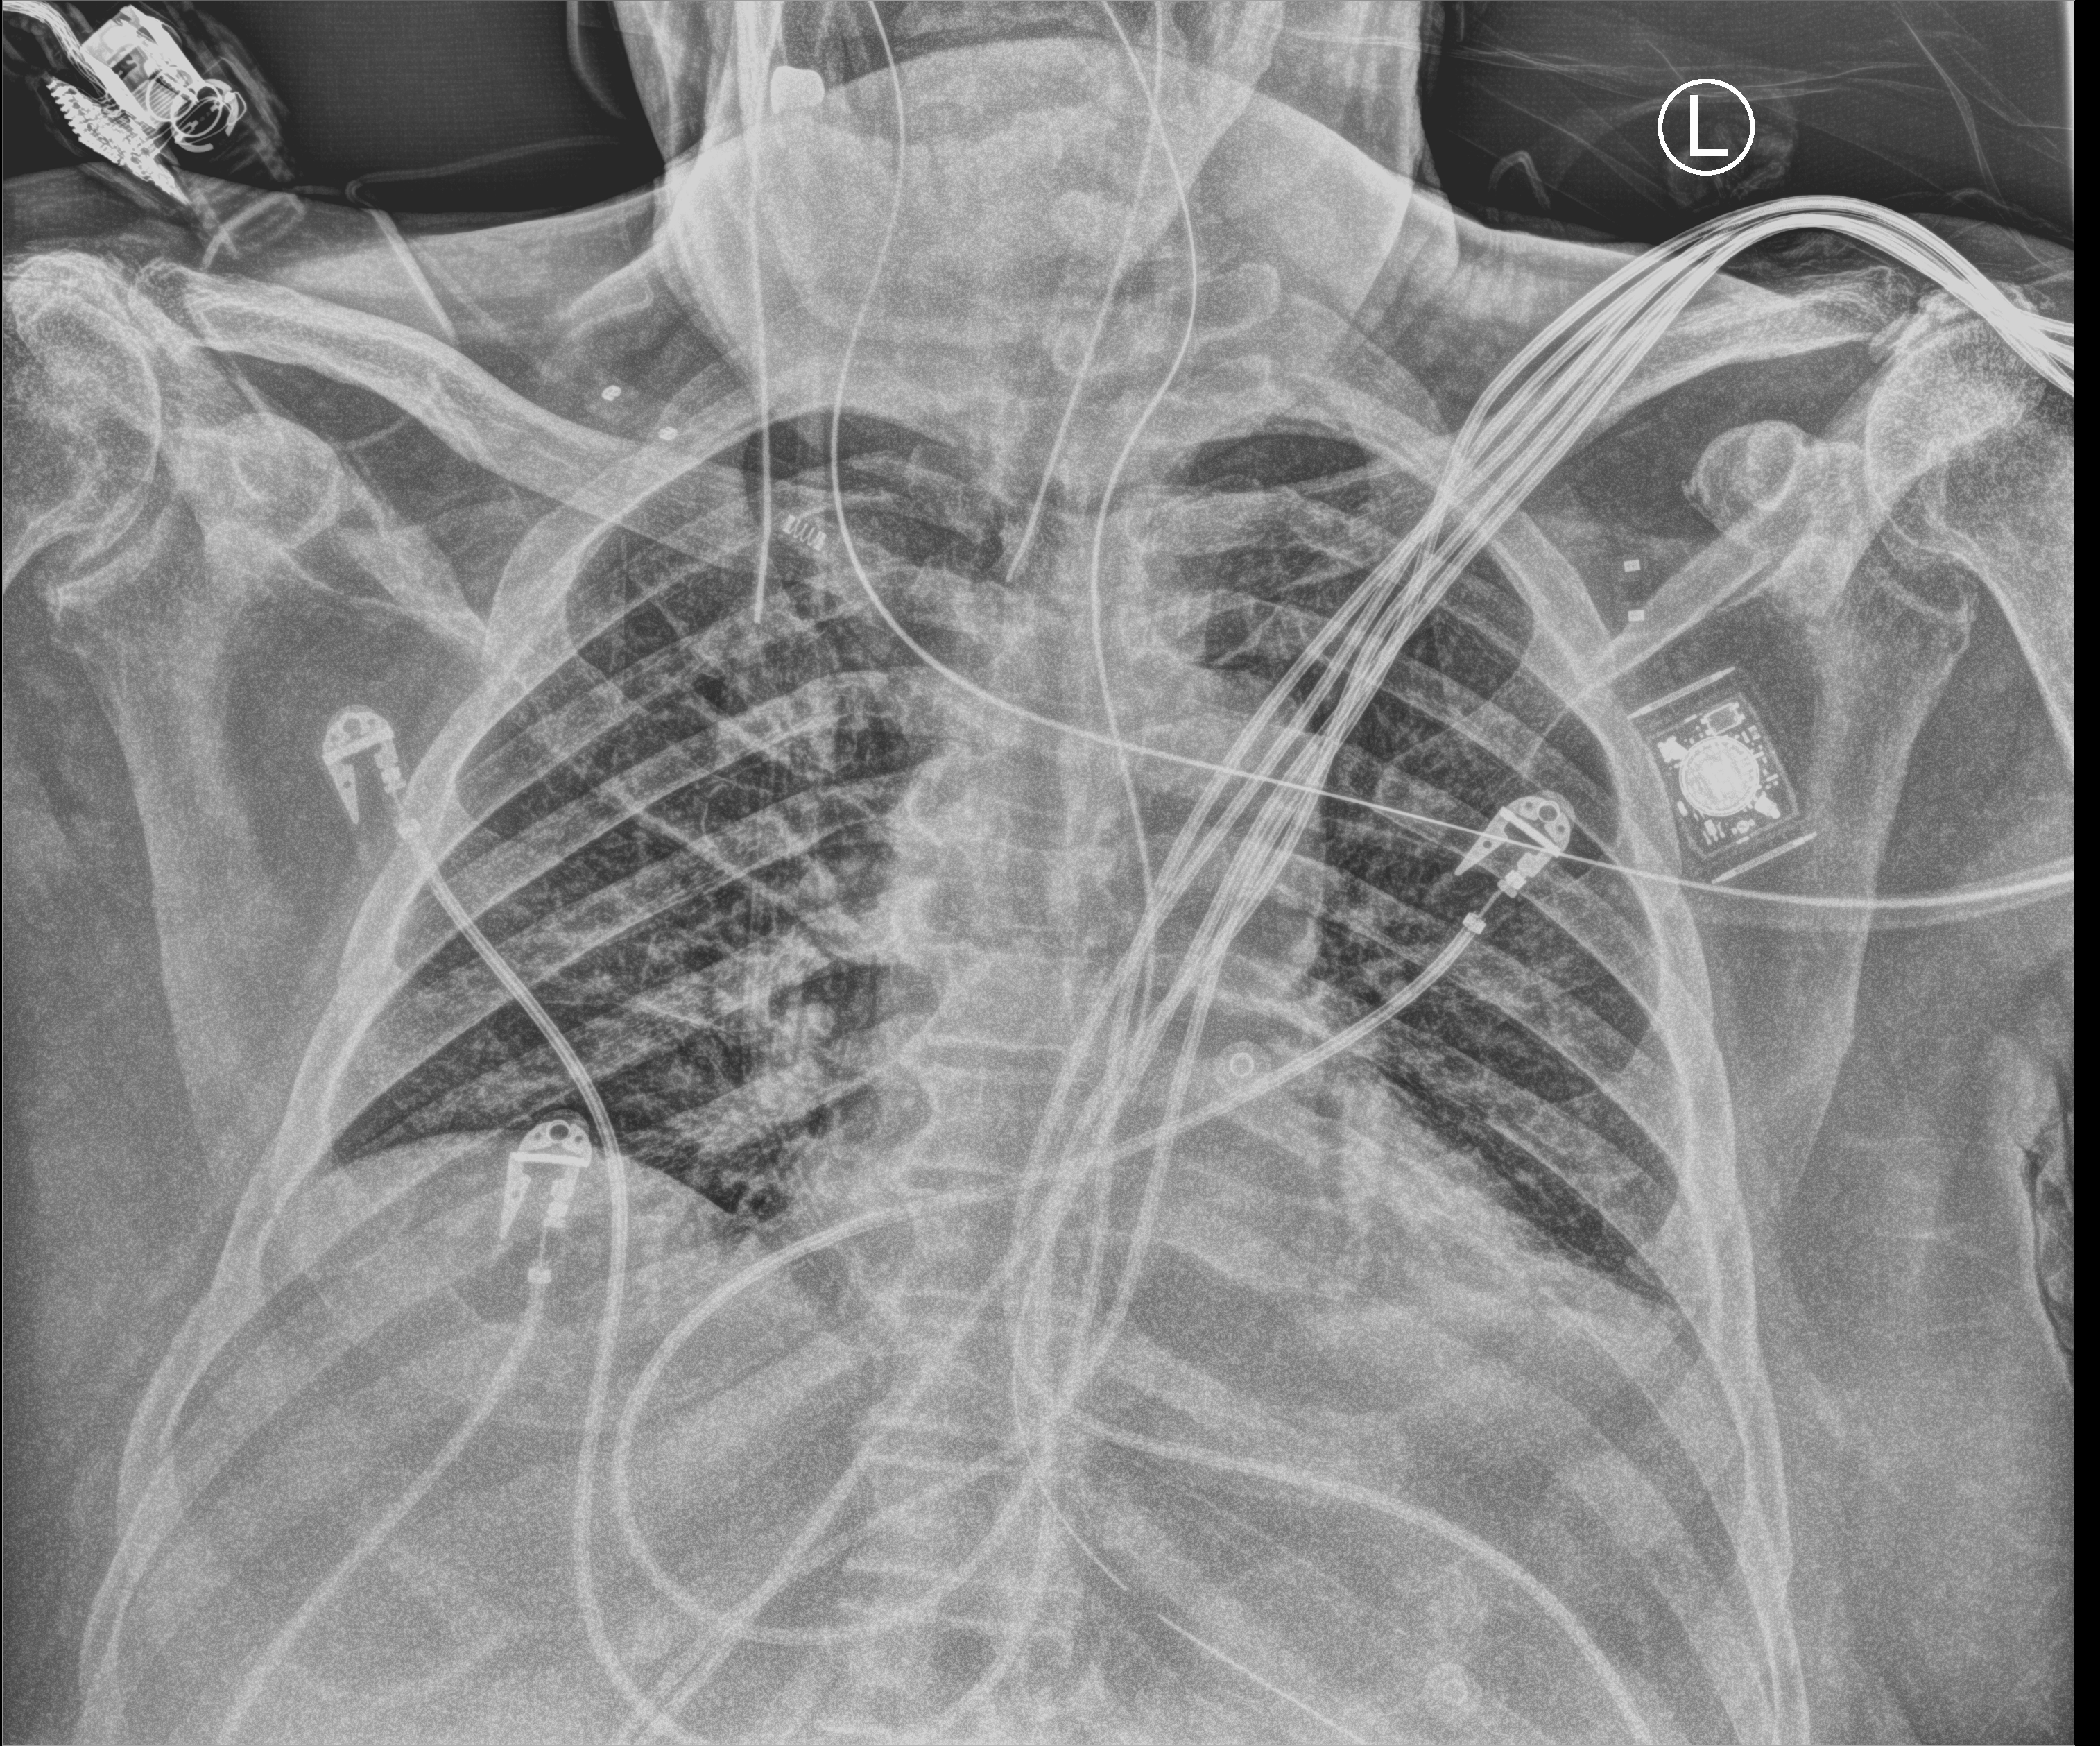
Bedside chest radiograph (computed radiography); anteroposterior (AP) projection. Male patient hospitalised with COVID-19, age 75–90 years.
Admission-level facts for this patient (not findings on this image; timing relative to this image not recorded):
- length of hospital stay: 12 days
- chronic kidney disease (admission record): no
- mechanically ventilated during this hospital stay: yes